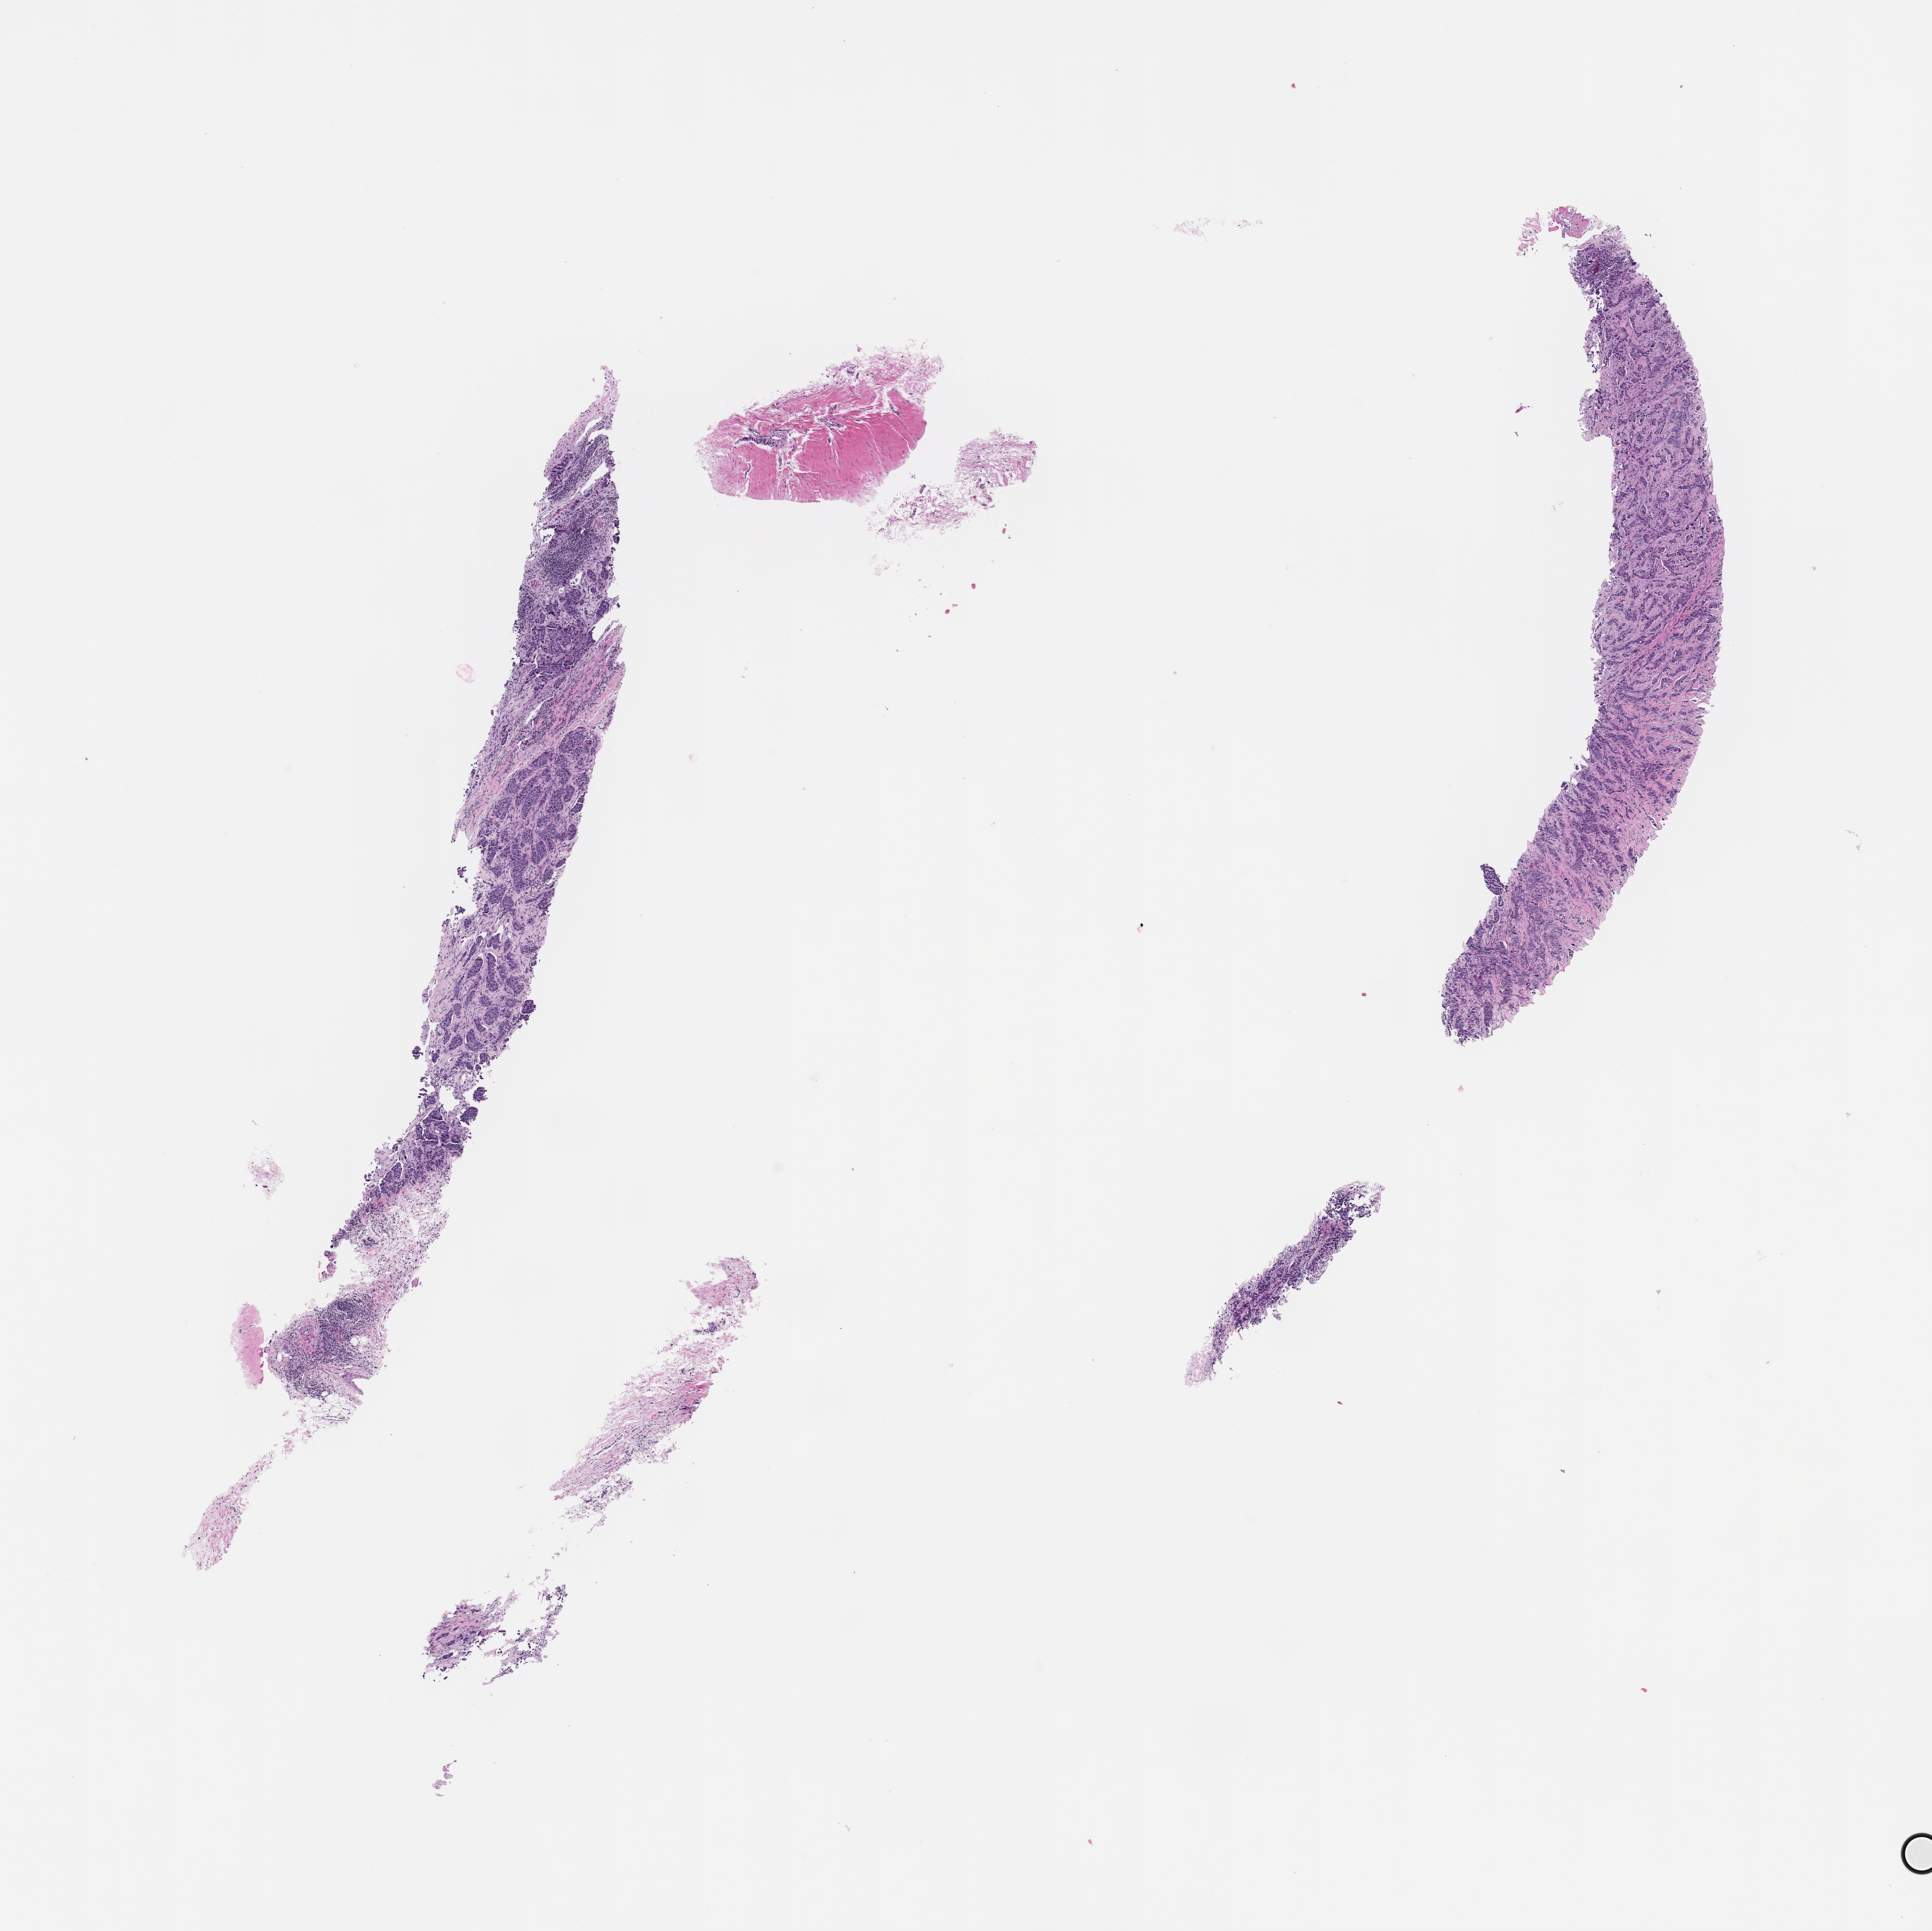
Haematoxylin and eosin whole-slide image, shown as a low-resolution overview of the whole scanned area (about 11.1 x 11.0 mm); formalin-fixed, paraffin-embedded (FFPE) tissue; specimen time point: archival tissue. Patient: female.
* this section: metastasis (sampled organ not recorded)
* patient diagnosis (primary): Invasive Breast Carcinoma